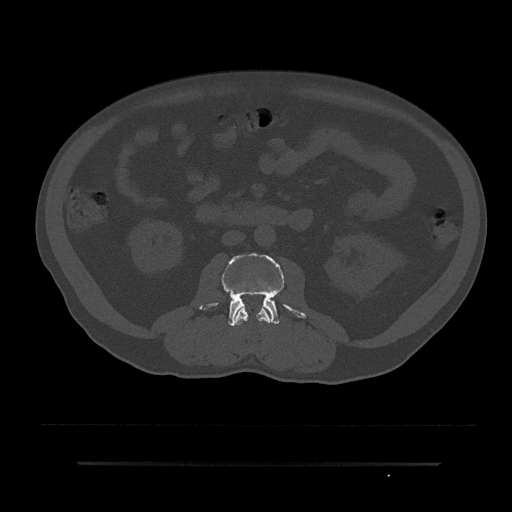
CT including the spine, one axial slice; slice 28 of 797 in the series (ordered by position); reconstruction kernel Br40s/3; 120 kVp; bone window (W 1800 / L 400 HU); 512 × 512 image matrix. Male patient, age 59 years. From the clinical record (not read from this slice): primary cancer: bile ducts; vertebrae with lytic lesions (as recorded): T10.
Outlined on this slice (semi-automatic segmentation, software-assisted and operator-edited):
- L2 vertebra: box from (x=233, y=304) to (x=273, y=325) px
- L3 vertebra: (x=200, y=253)–(x=306, y=326)